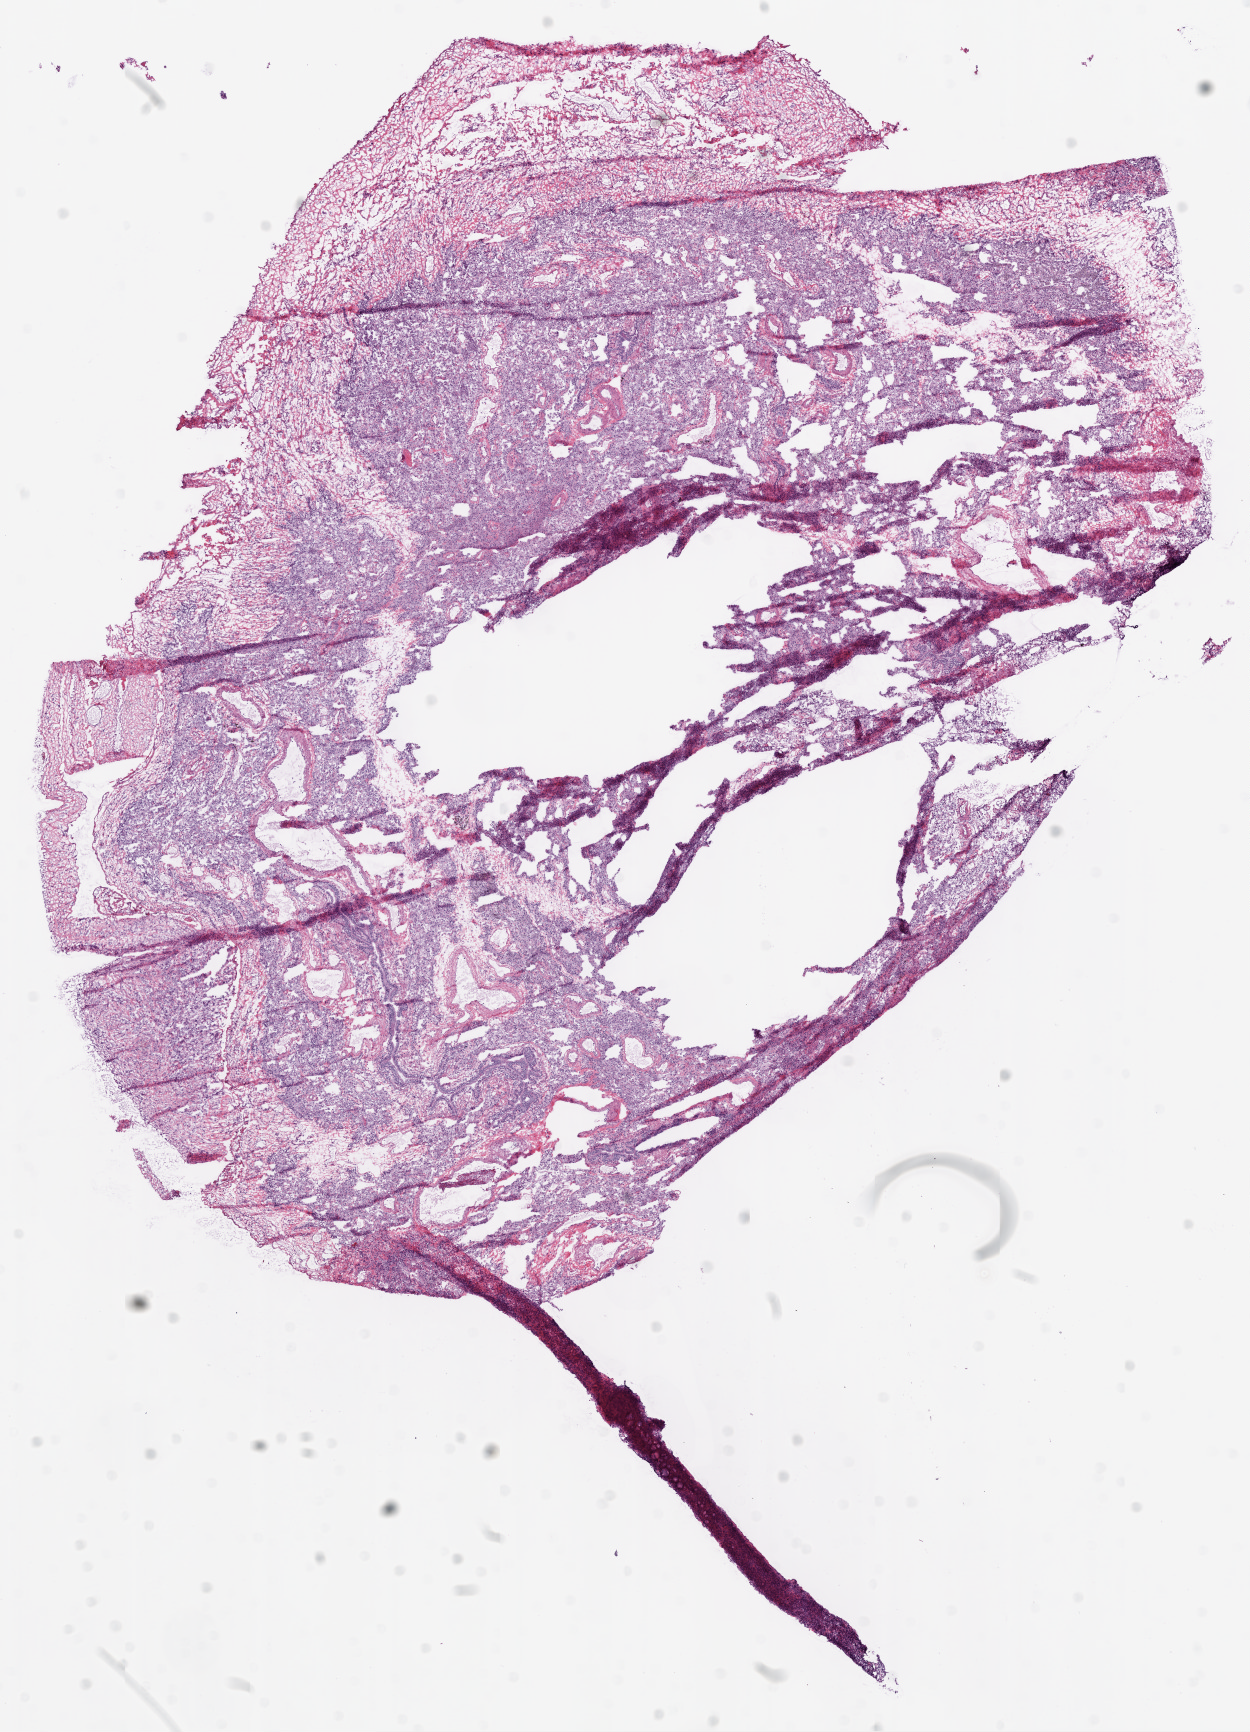
H&E whole-slide image, shown as a low-resolution overview of the whole scanned area (about 10.0 x 13.9 mm, slide scanned at 20x); frozen section; sample: solid tissue normal (non-tumour tissue), lung. Patient: male, age at initial diagnosis 57 years.
This section: solid tissue normal (non-tumour) sample from the same patient. Patient diagnosis: Squamous cell carcinoma, NOS (lower lobe, lung).